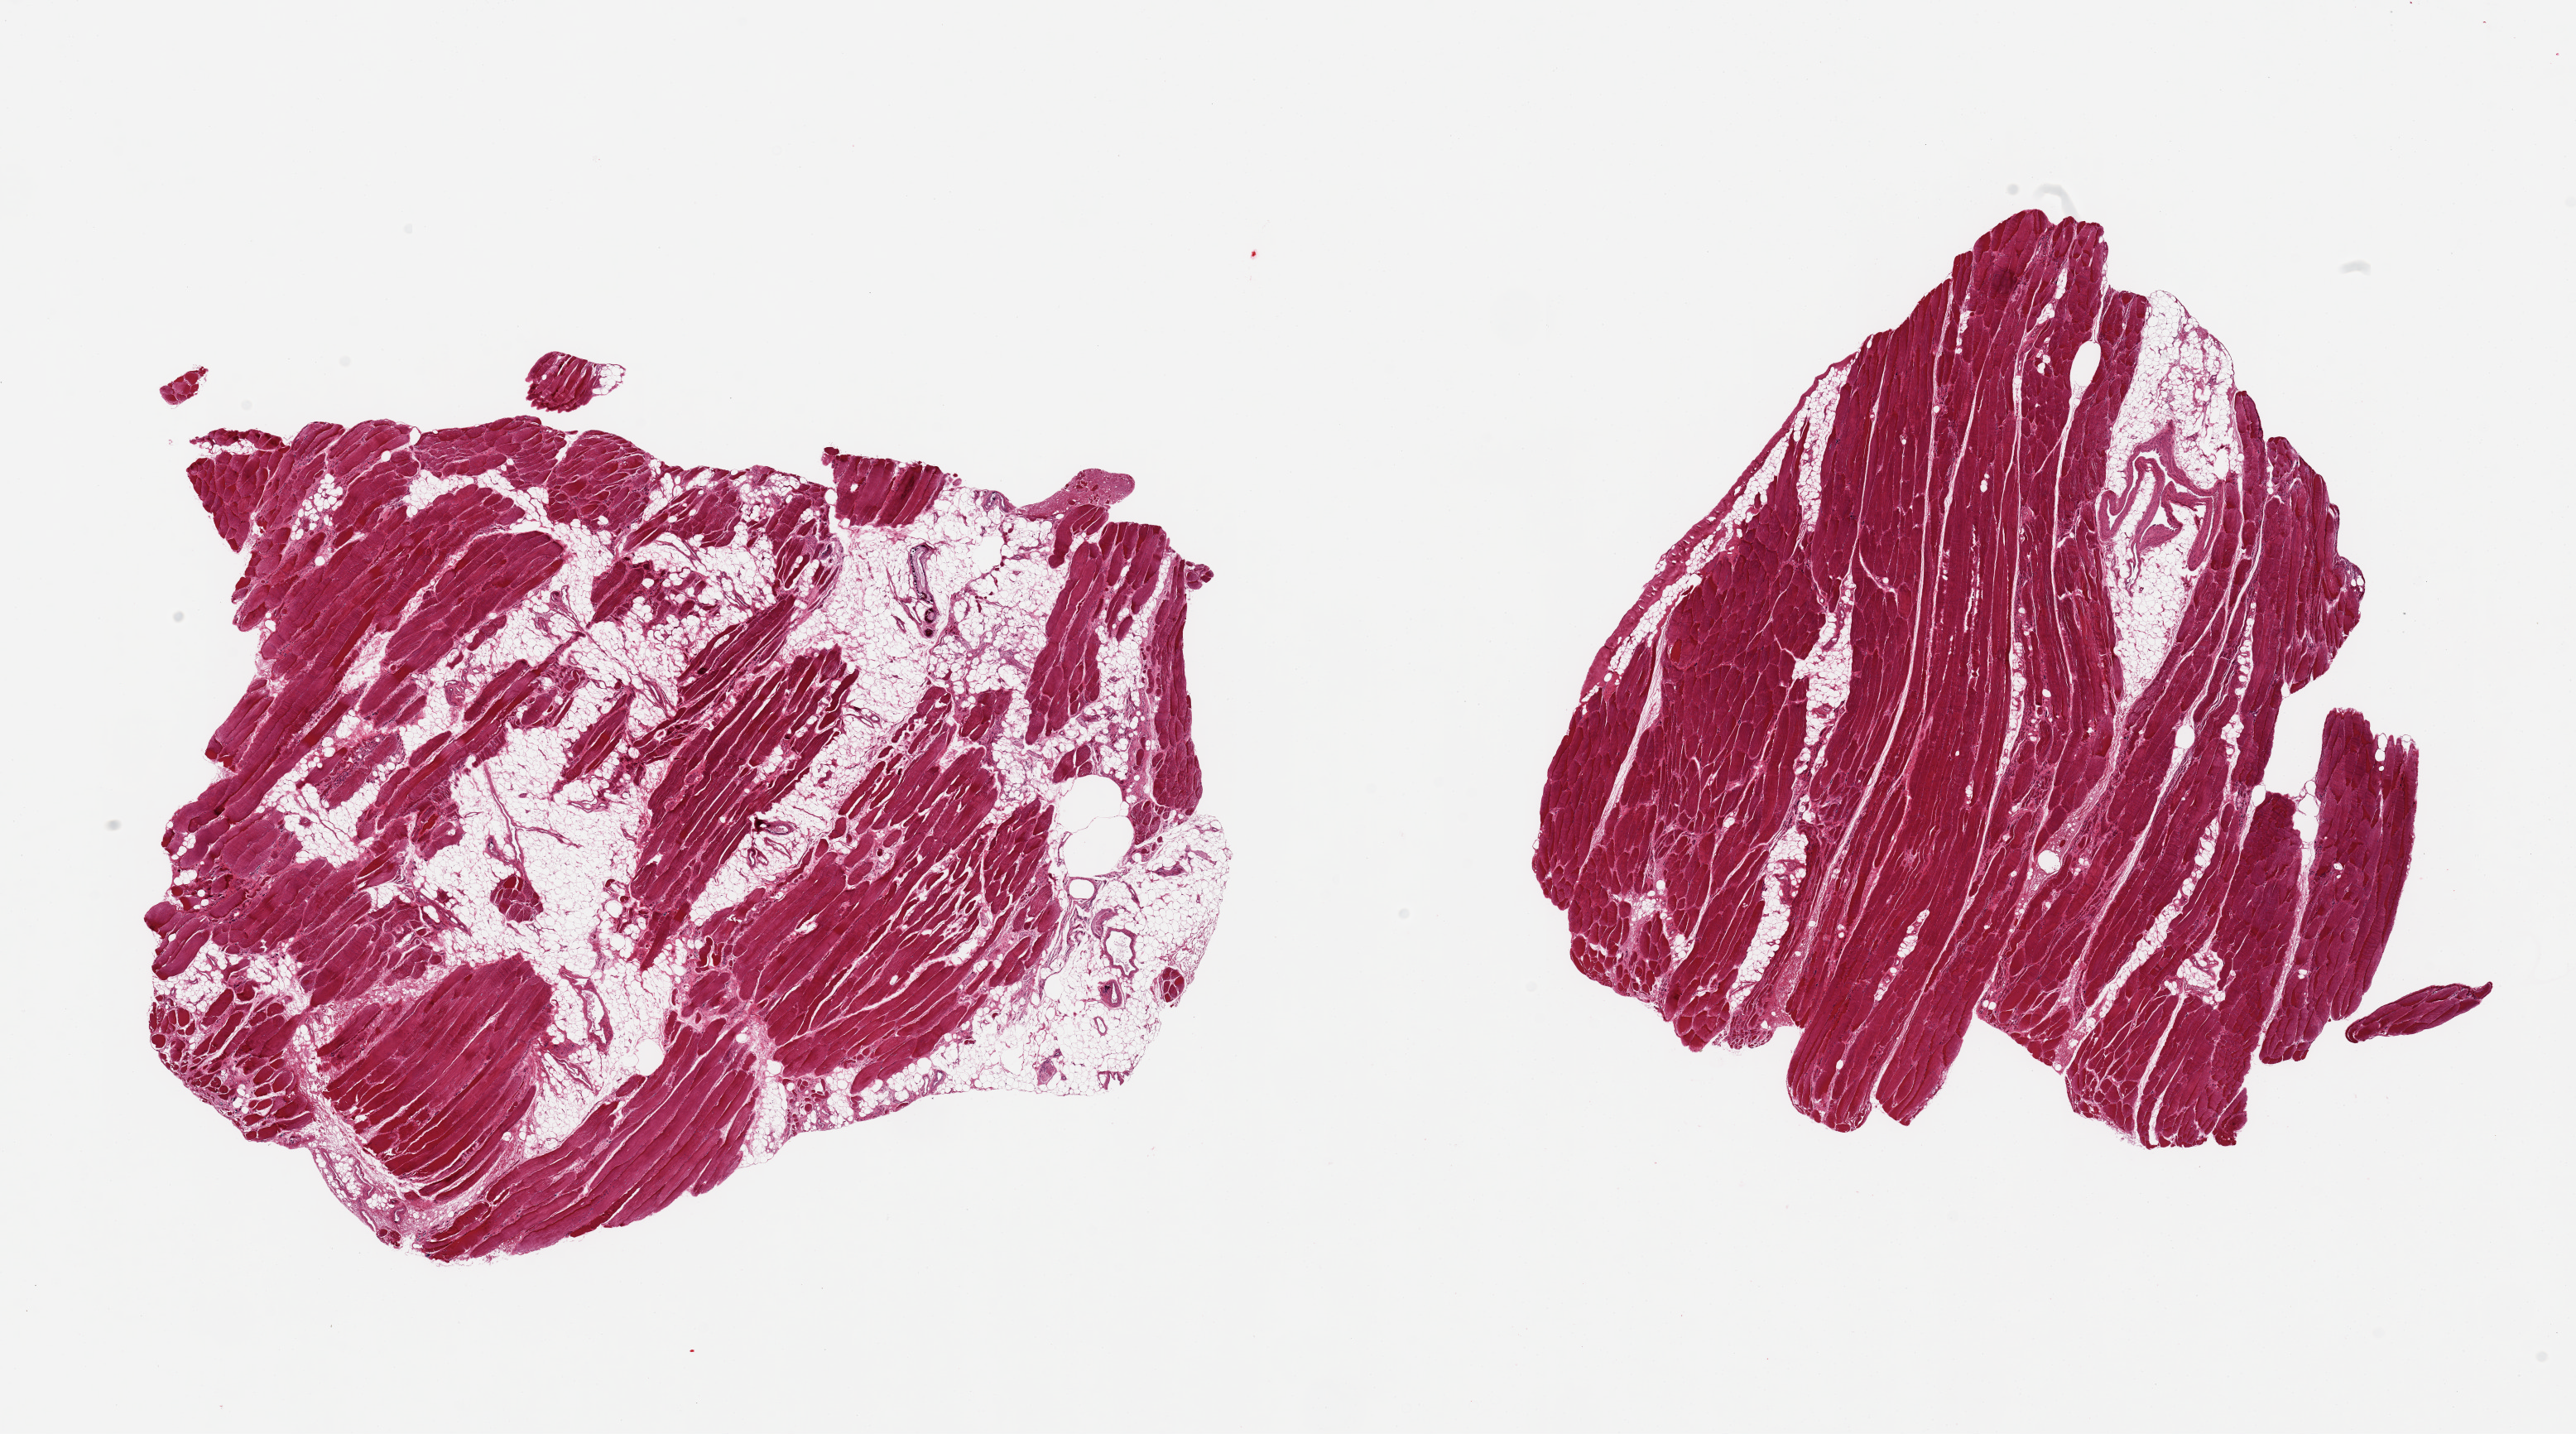
Hematoxylin and eosin (H&E) whole-slide image, a low-resolution overview of the entire scanned area, about 24.6 x 13.7 mm. PAXgene-fixed paraffin-embedded (PFPE) section. Sampled site (target tissue): skeletal muscle. Tissue donor sample. Donor sex: male.
Pathologist's review note for this sample: 2 pieces; includes 10 and 50% attached and internal fat, some atrophic fibers, medial calcification of vessels.